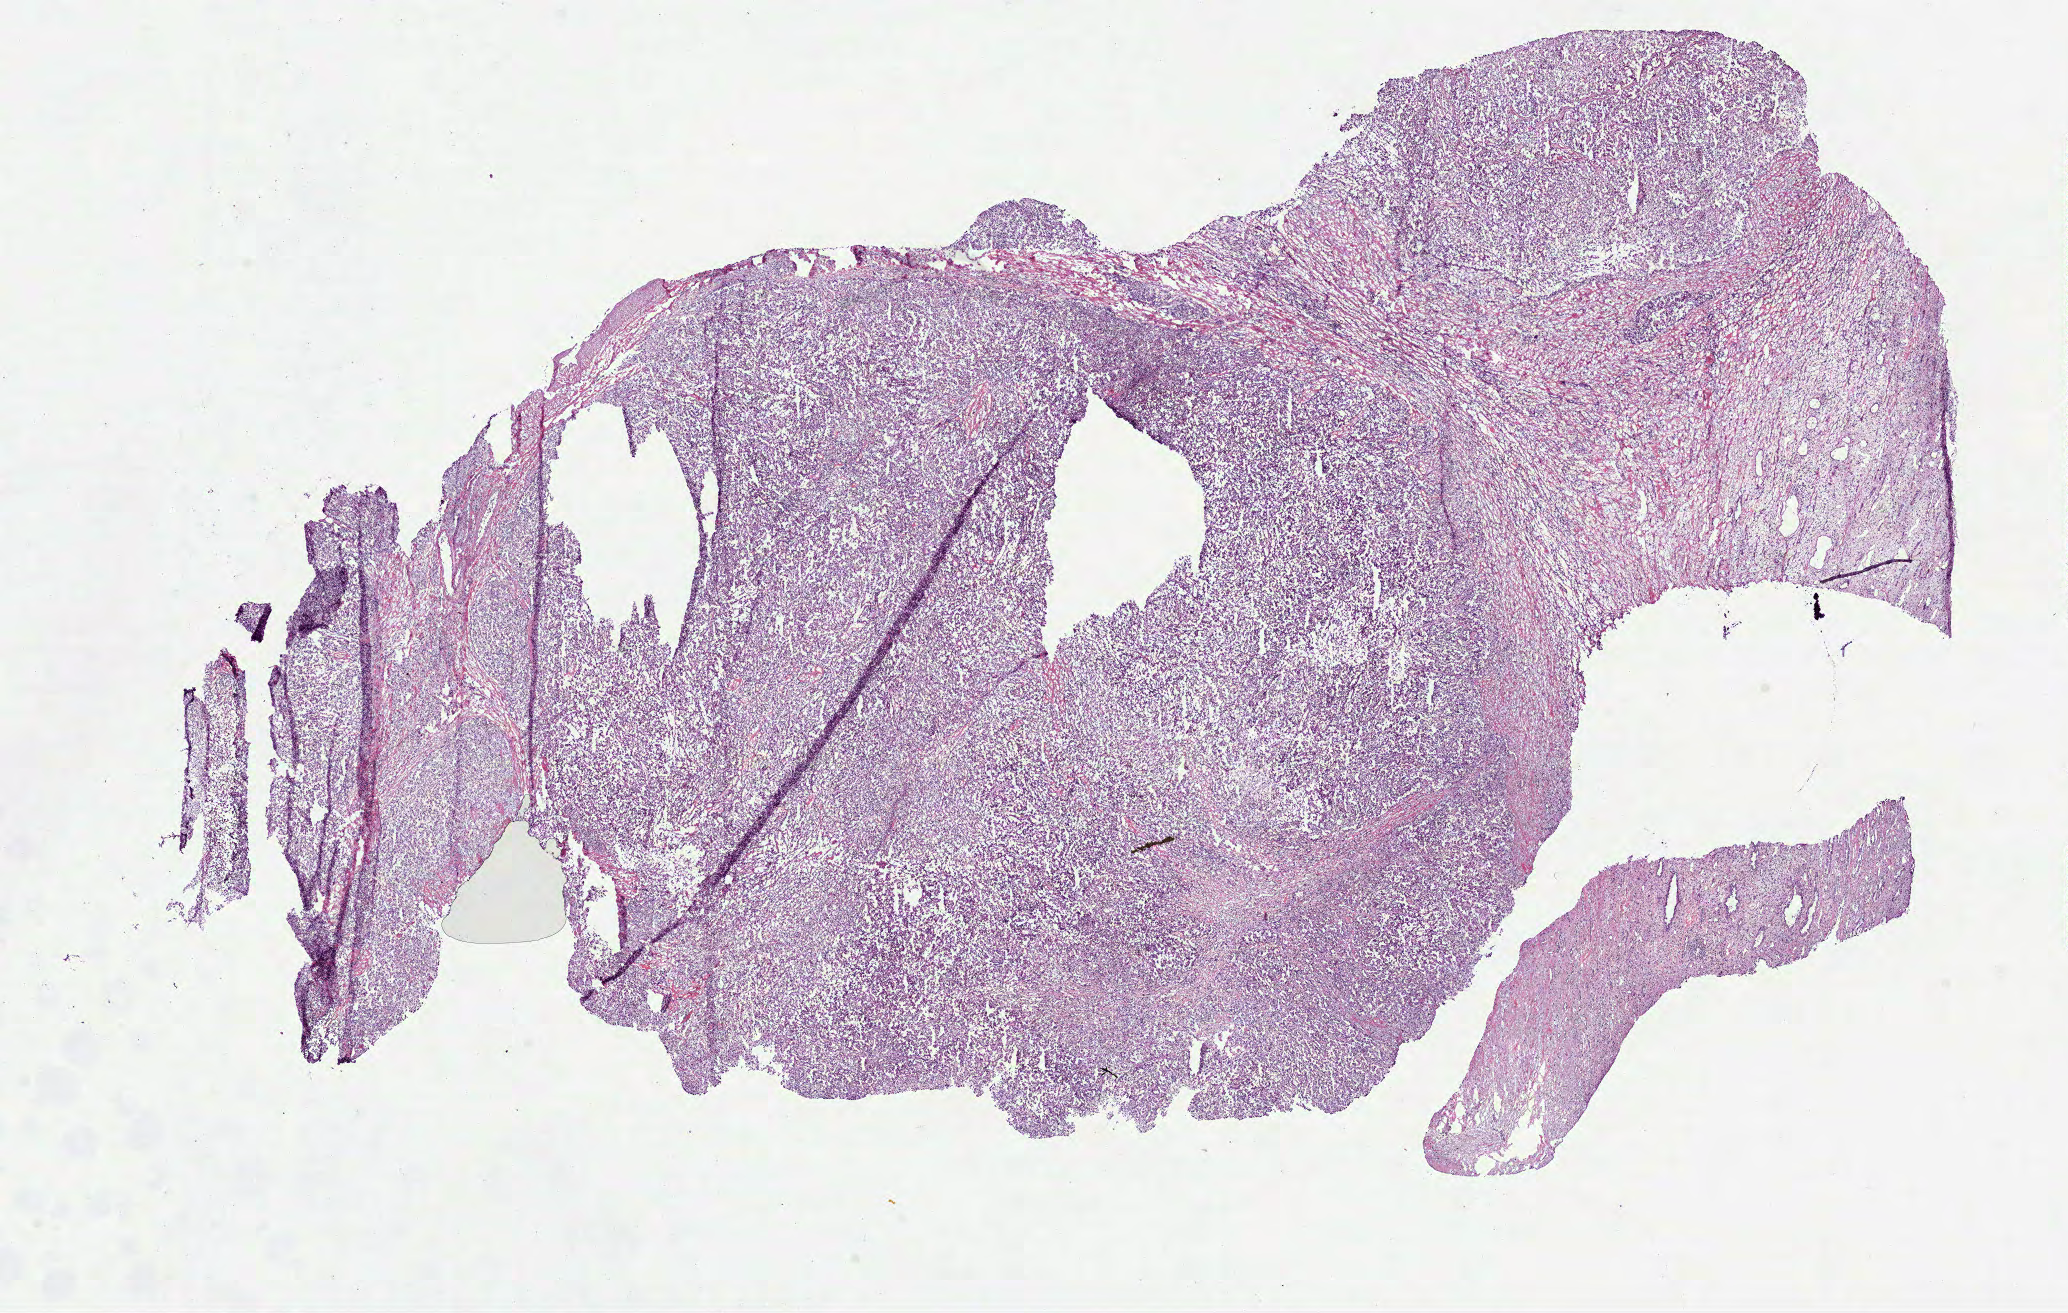
Whole-slide histology image, H&E, a low-resolution overview of the entire scanned area, about 16.7 x 10.6 mm. Frozen section from the bottom of the tissue portion. Primary tumour sample from the kidney. Male, age 60 years at initial diagnosis. Slide review estimates, as recorded: tumour cells 70%, tumour nuclei 78%.
Diagnosis: Papillary adenocarcinoma, NOS.